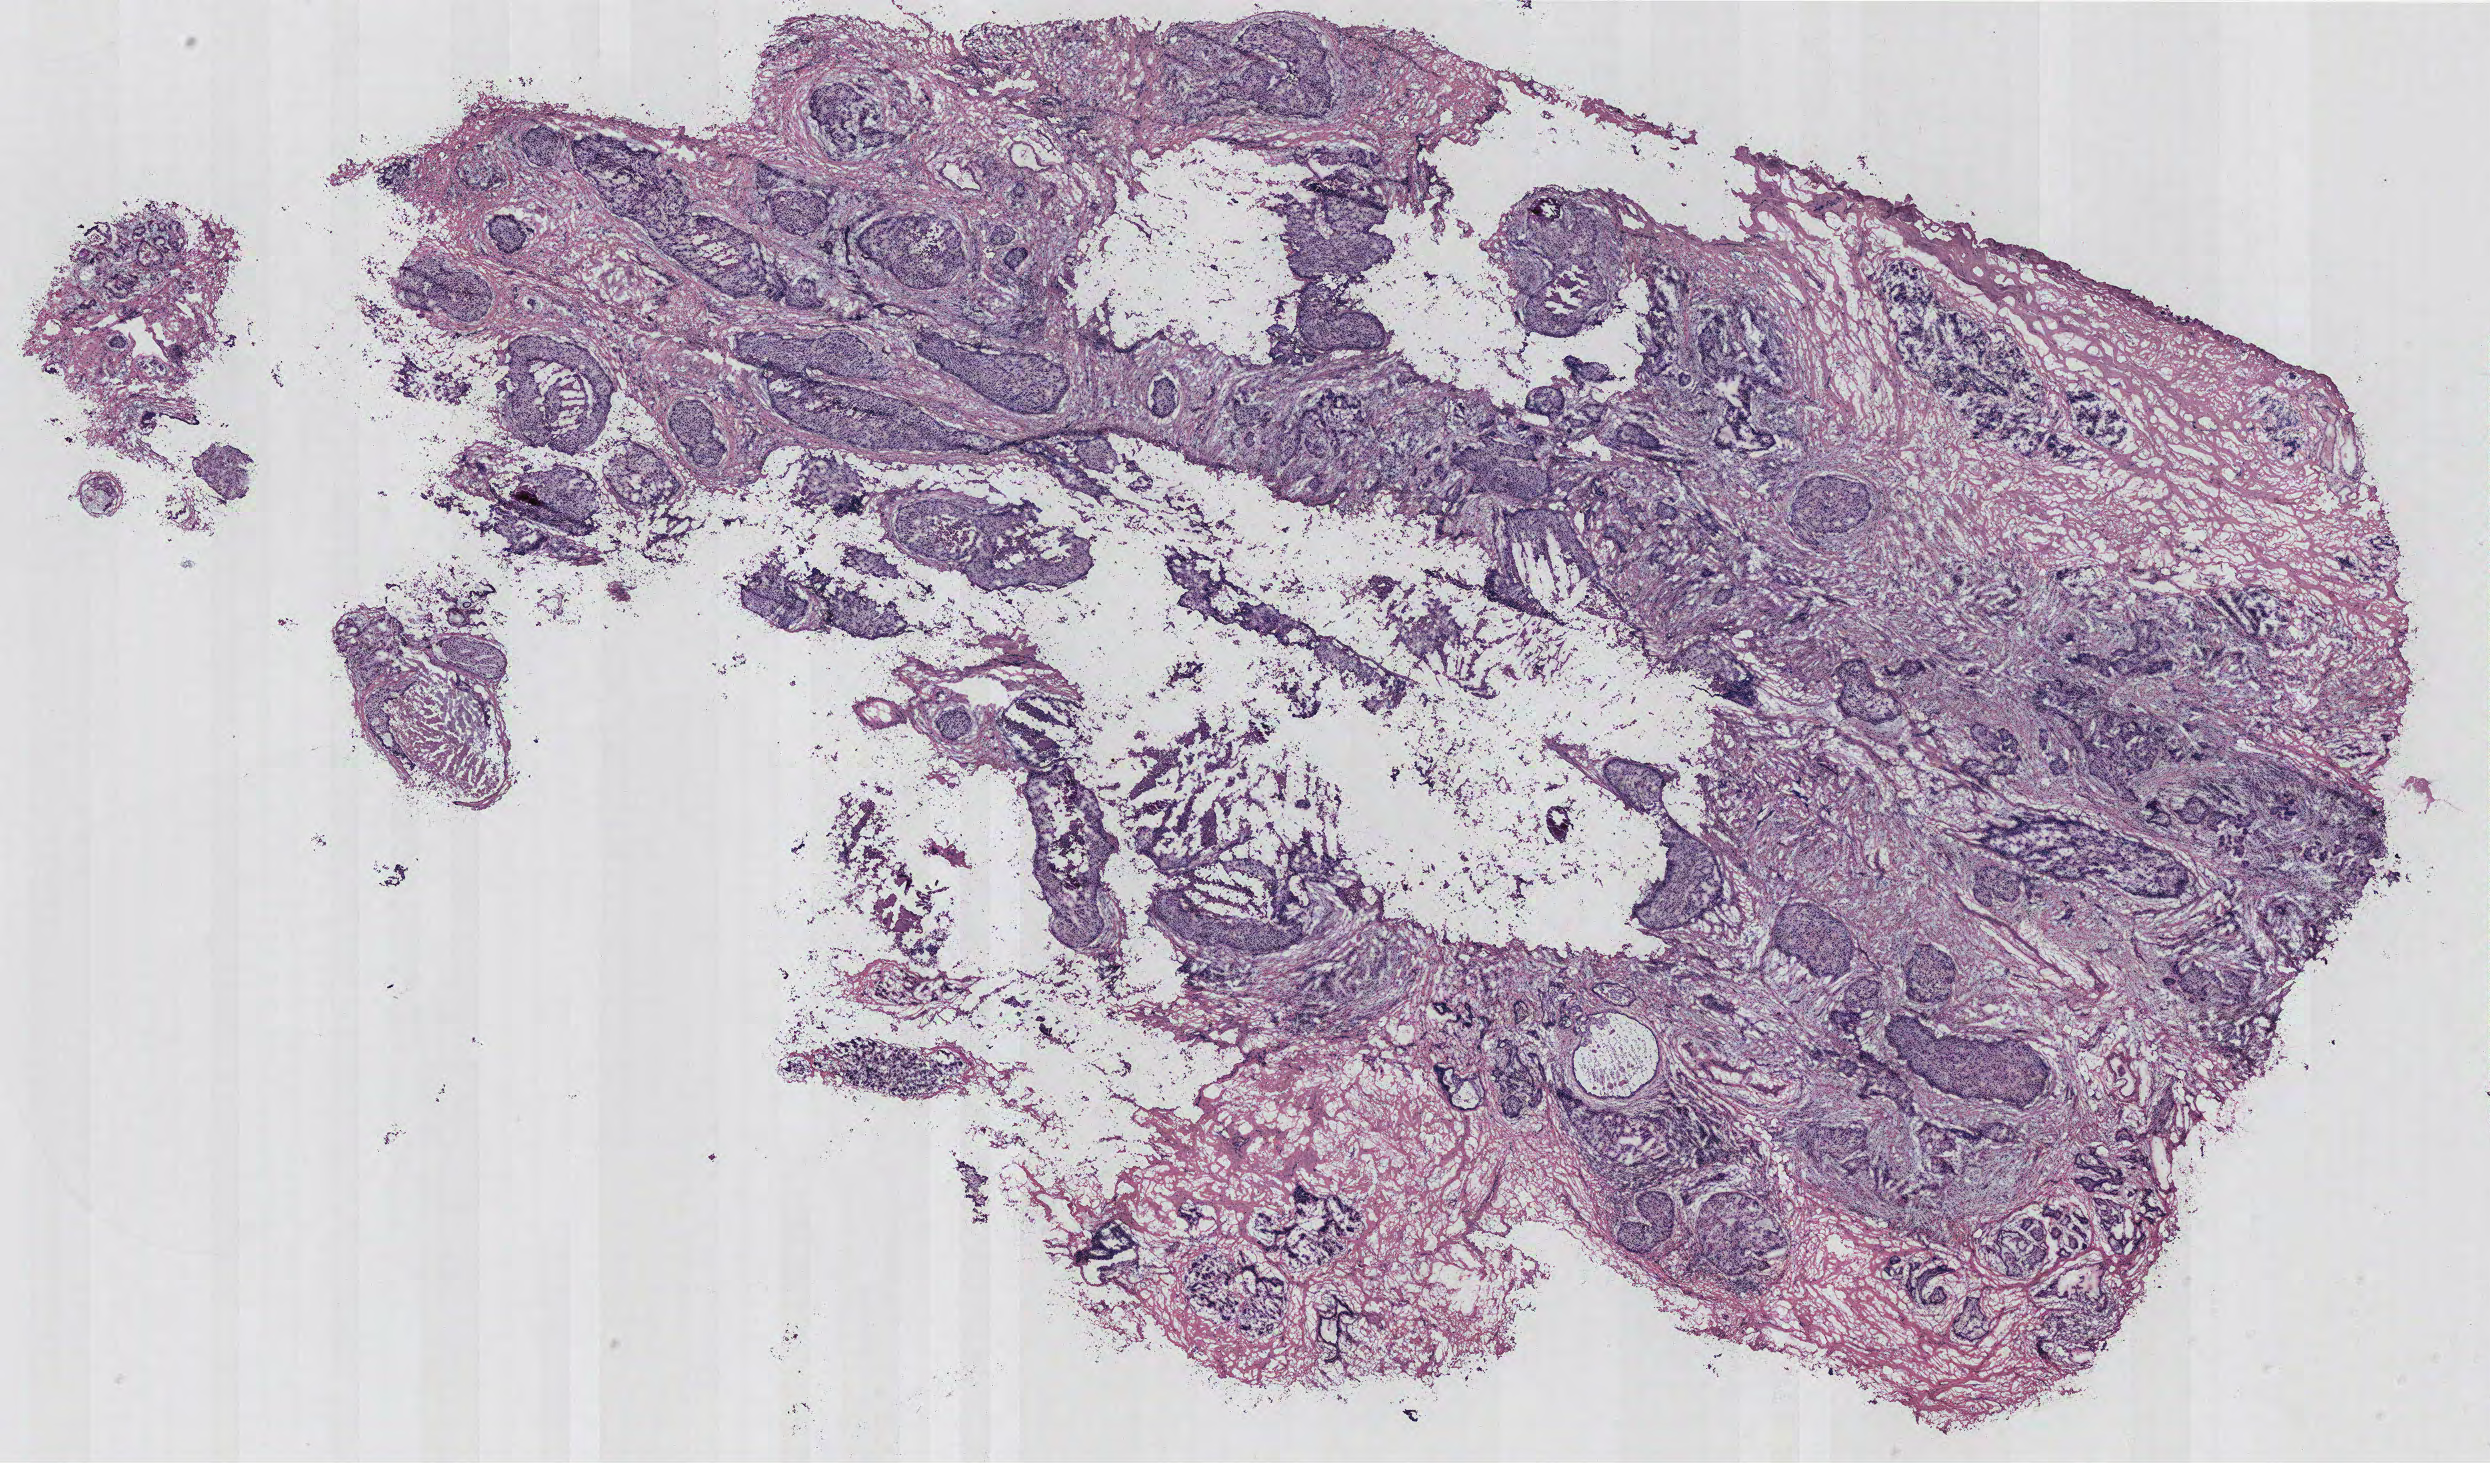
Whole-slide histology image, H&E, a low-resolution overview of the entire scanned area, about 19.9 x 11.7 mm, breast, tissue type not recorded. 45-year-old female patient.
- patient diagnosis: Infiltrating duct carcinoma, NOS